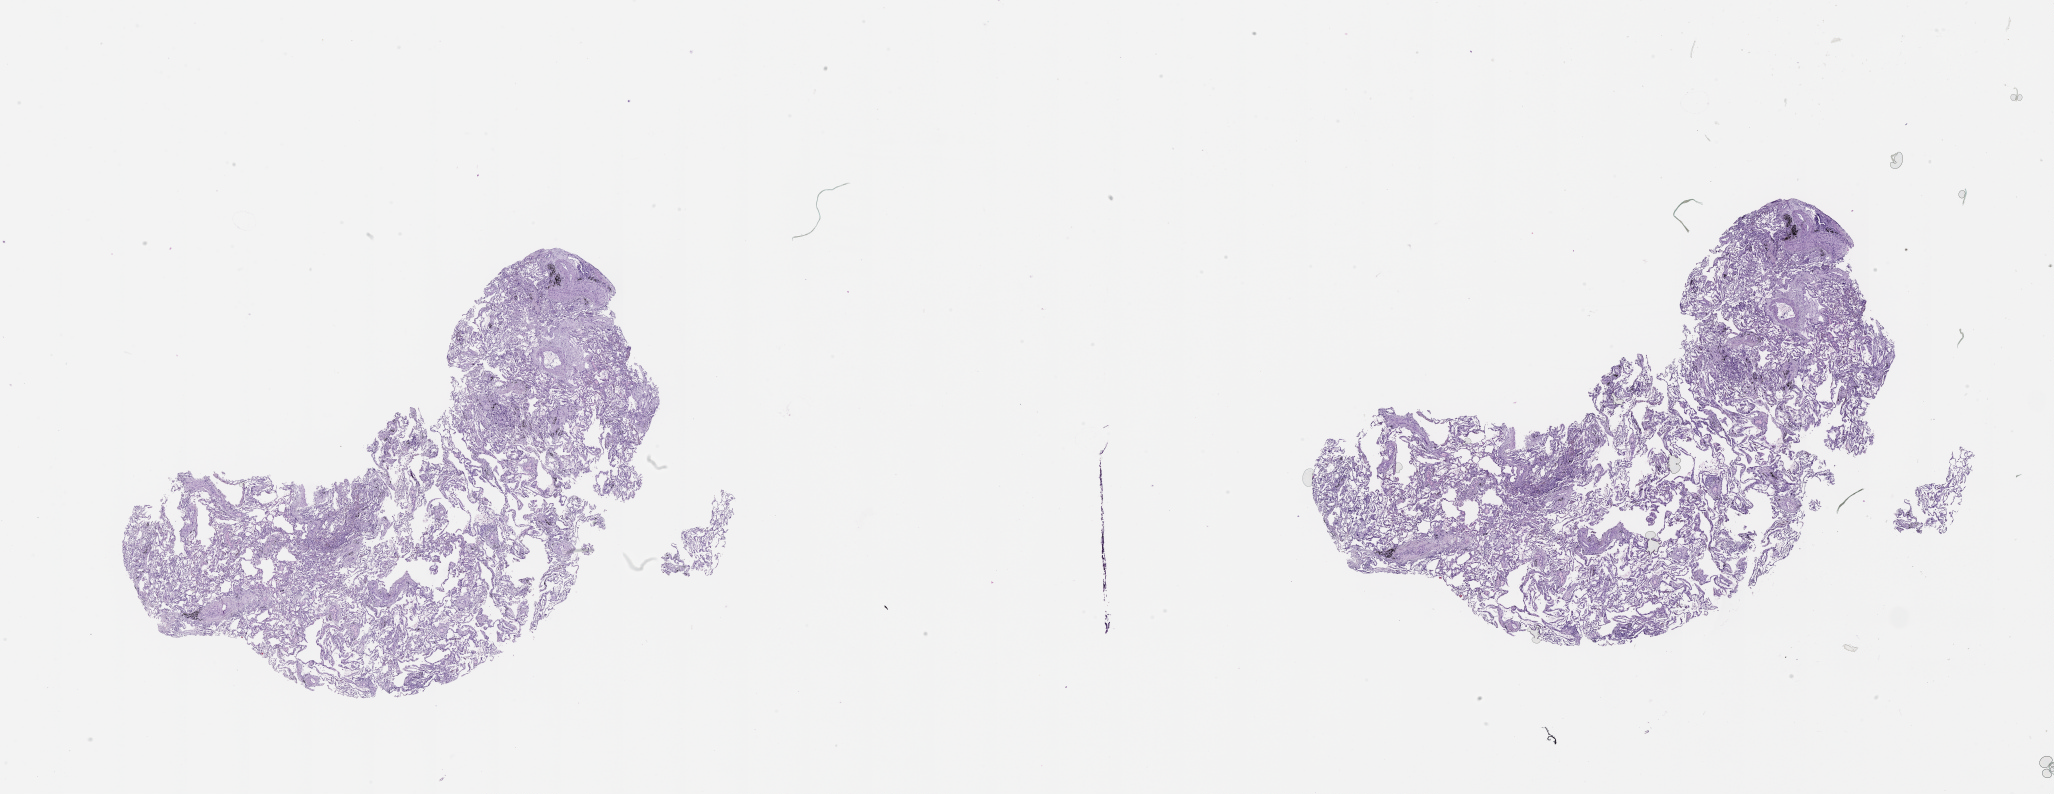
H&E-stained whole-slide image, shown as a low-resolution overview of the whole scanned area (about 33.1 x 12.8 mm), lung, normal (non-tumour) tissue. Male, 63 y/o.
This section: normal (non-tumour) tissue from the same patient. Patient diagnosis (cohort enrolment): squamous cell carcinoma (lung).